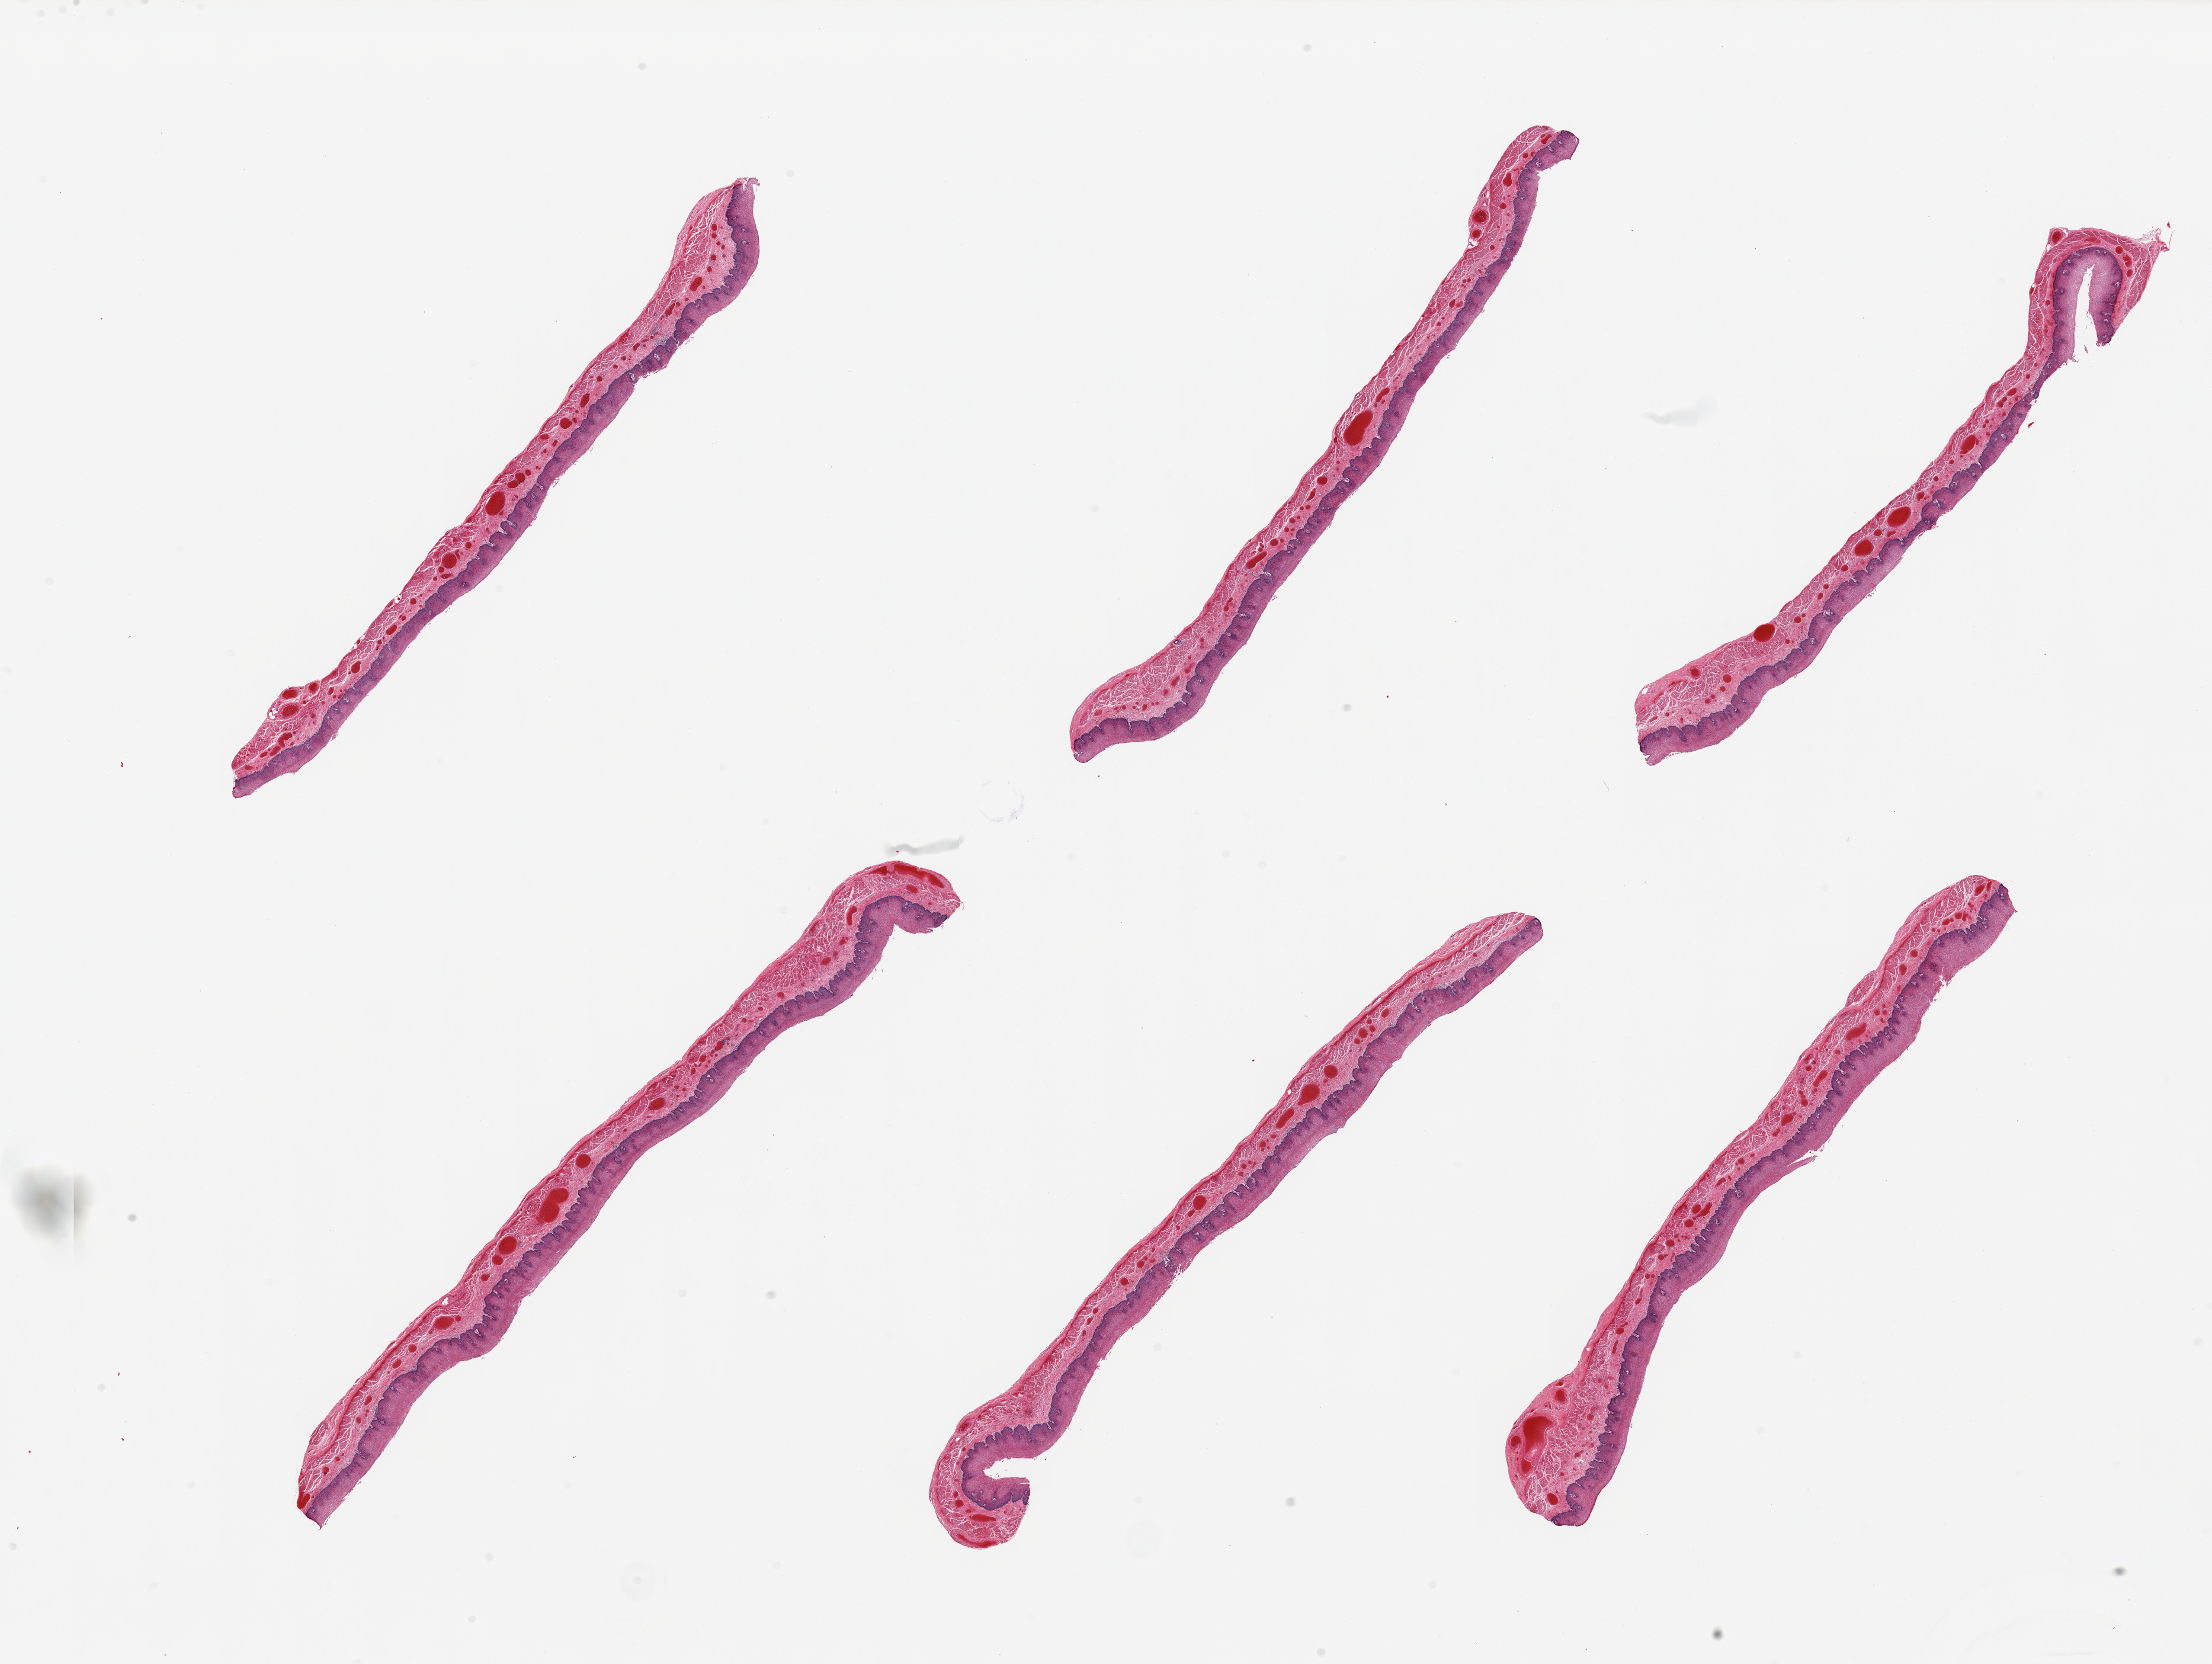
Digitized hematoxylin and eosin (H&E)-stained section, low-resolution overview of the scanned area, about 29.5 x 22.2 mm (acquisition: 20x scan); PAXgene-fixed paraffin-embedded (PFPE) section; sampled site (target tissue): esophageal mucous membrane; donor tissue sample. Donor sex: male.
- review note (as recorded): 6 pieces; congested vessels